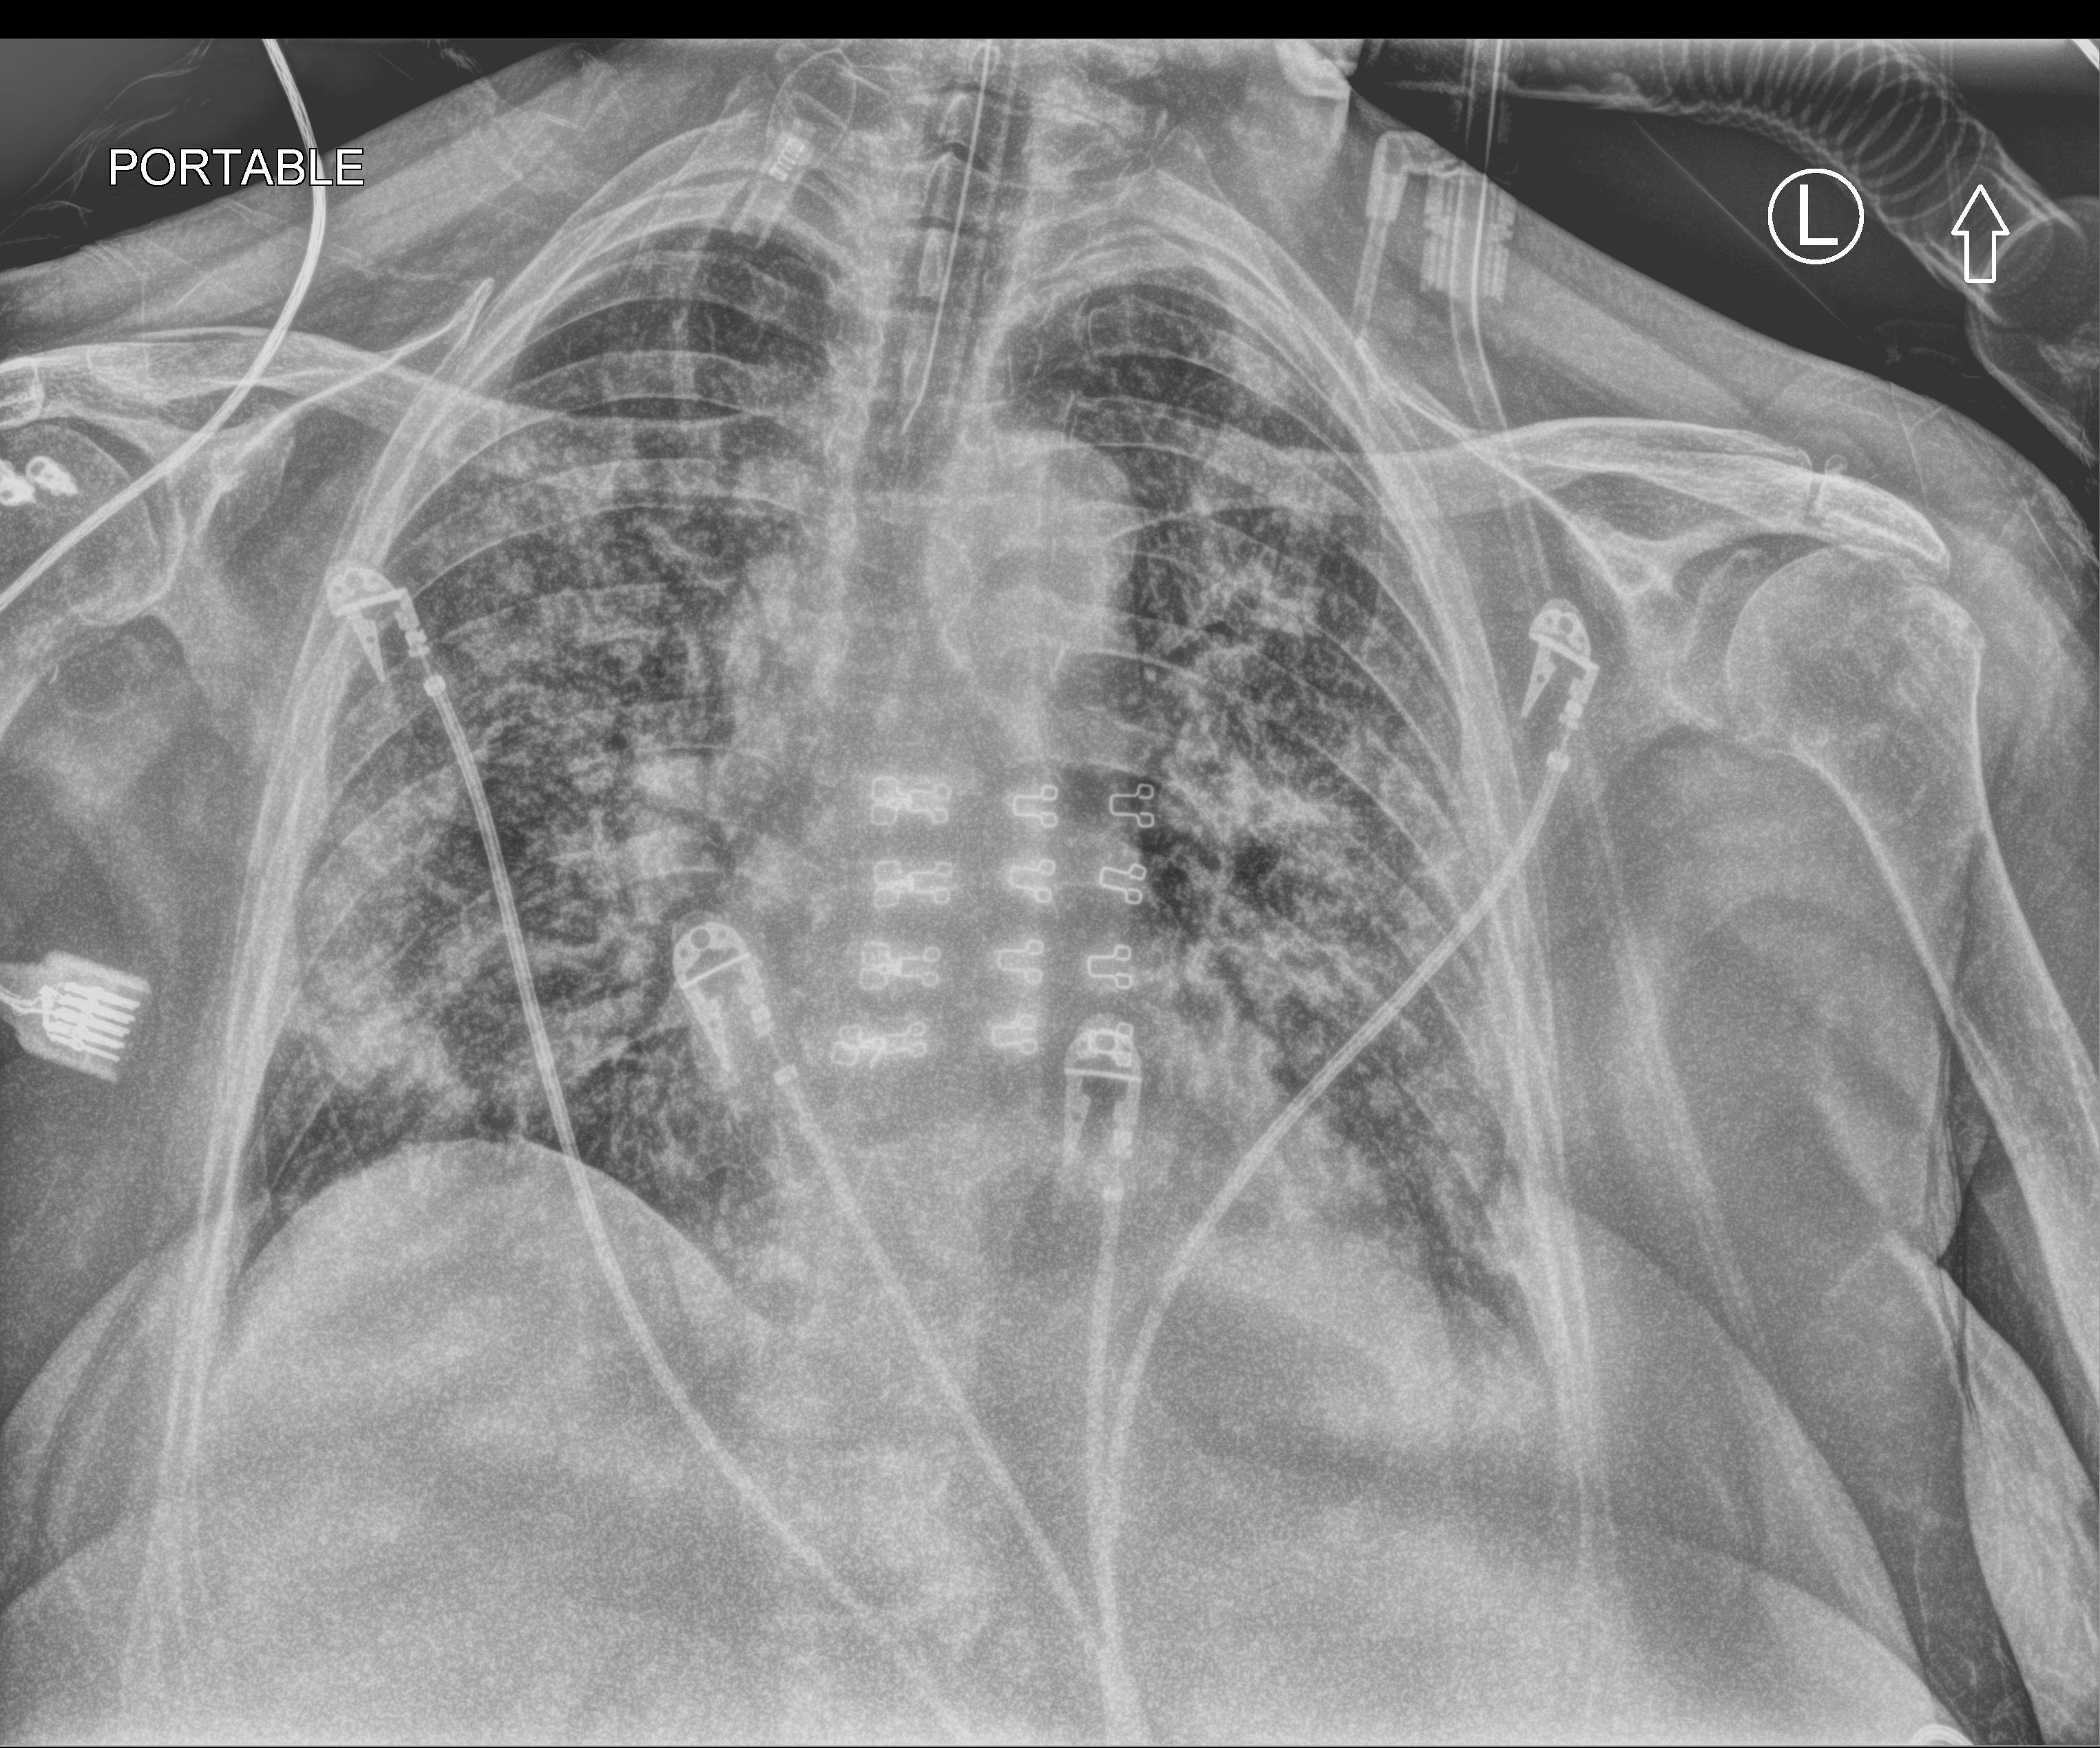
Bedside chest radiograph (computed radiography), anteroposterior (AP) projection. Patient hospitalised with COVID-19; female, aged 60–74 years.
From the hospital-stay record, not from the radiograph (when in the stay this image was taken is not recorded):
- admitted to intensive care during this hospital stay: yes
- mechanically ventilated during this hospital stay: yes
- diabetes (admission record): no